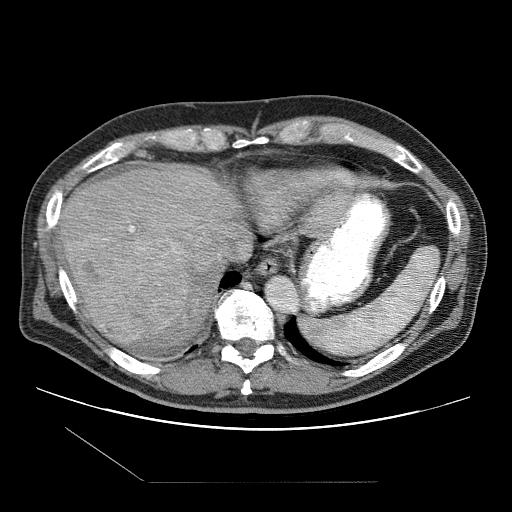
Contrast-enhanced abdominal CT (liver protocol), one axial slice; position 84 of 109 along the scan axis; one of 2 acquisitions stored at this slice position; soft-tissue window (W 400 / L 40 HU); 512 × 512 image matrix, field of view 400 × 400 mm. Case-level facts recorded for this patient, not image findings: diagnosis: hepatocellular carcinoma (patient treated with transarterial chemoembolisation; whether this scan precedes or follows treatment is not stated here); TNM stage (as recorded): Stage-IIIB; Child-Pugh class: A; tumour differentiation: well differentiated; tumour nodularity: multinodular.
Annotated regions visible in this slice (semi-automatic segmentation, software-assisted and operator-edited):
- liver parenchyma outside the tumour (the mass and vessels are separate outlines, so this box may not span the whole liver): box from (x=58, y=164) to (x=252, y=345) px
- mass: (x=65, y=230)–(x=194, y=346)
- liver vessels: (x=129, y=226)–(x=134, y=232)